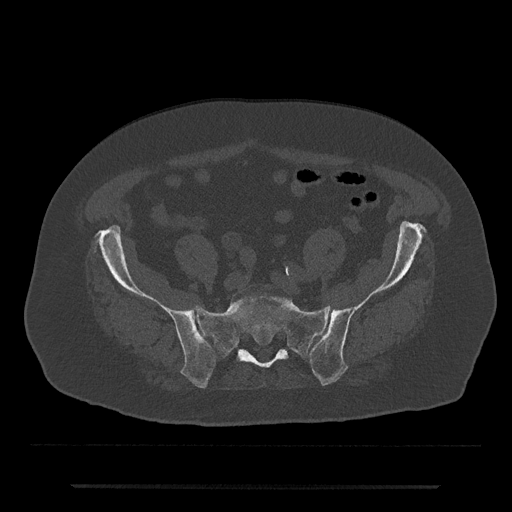
CT including the spine, one axial slice. Slice 229 of 797 in the series (ordered by position). Reconstruction kernel Br40s/3. 120 kVp. Bone window (W 1800 / L 400 HU). 512 × 512 image matrix. Patient: male, 80 years. Case-level facts recorded for this patient, not image findings: primary cancer: prostate.
Outlined on this slice (semi-automatic segmentation, software-assisted and operator-edited):
- L5 vertebra: bounding box [x1, y1, x2, y2] px = [261, 296, 265, 297]